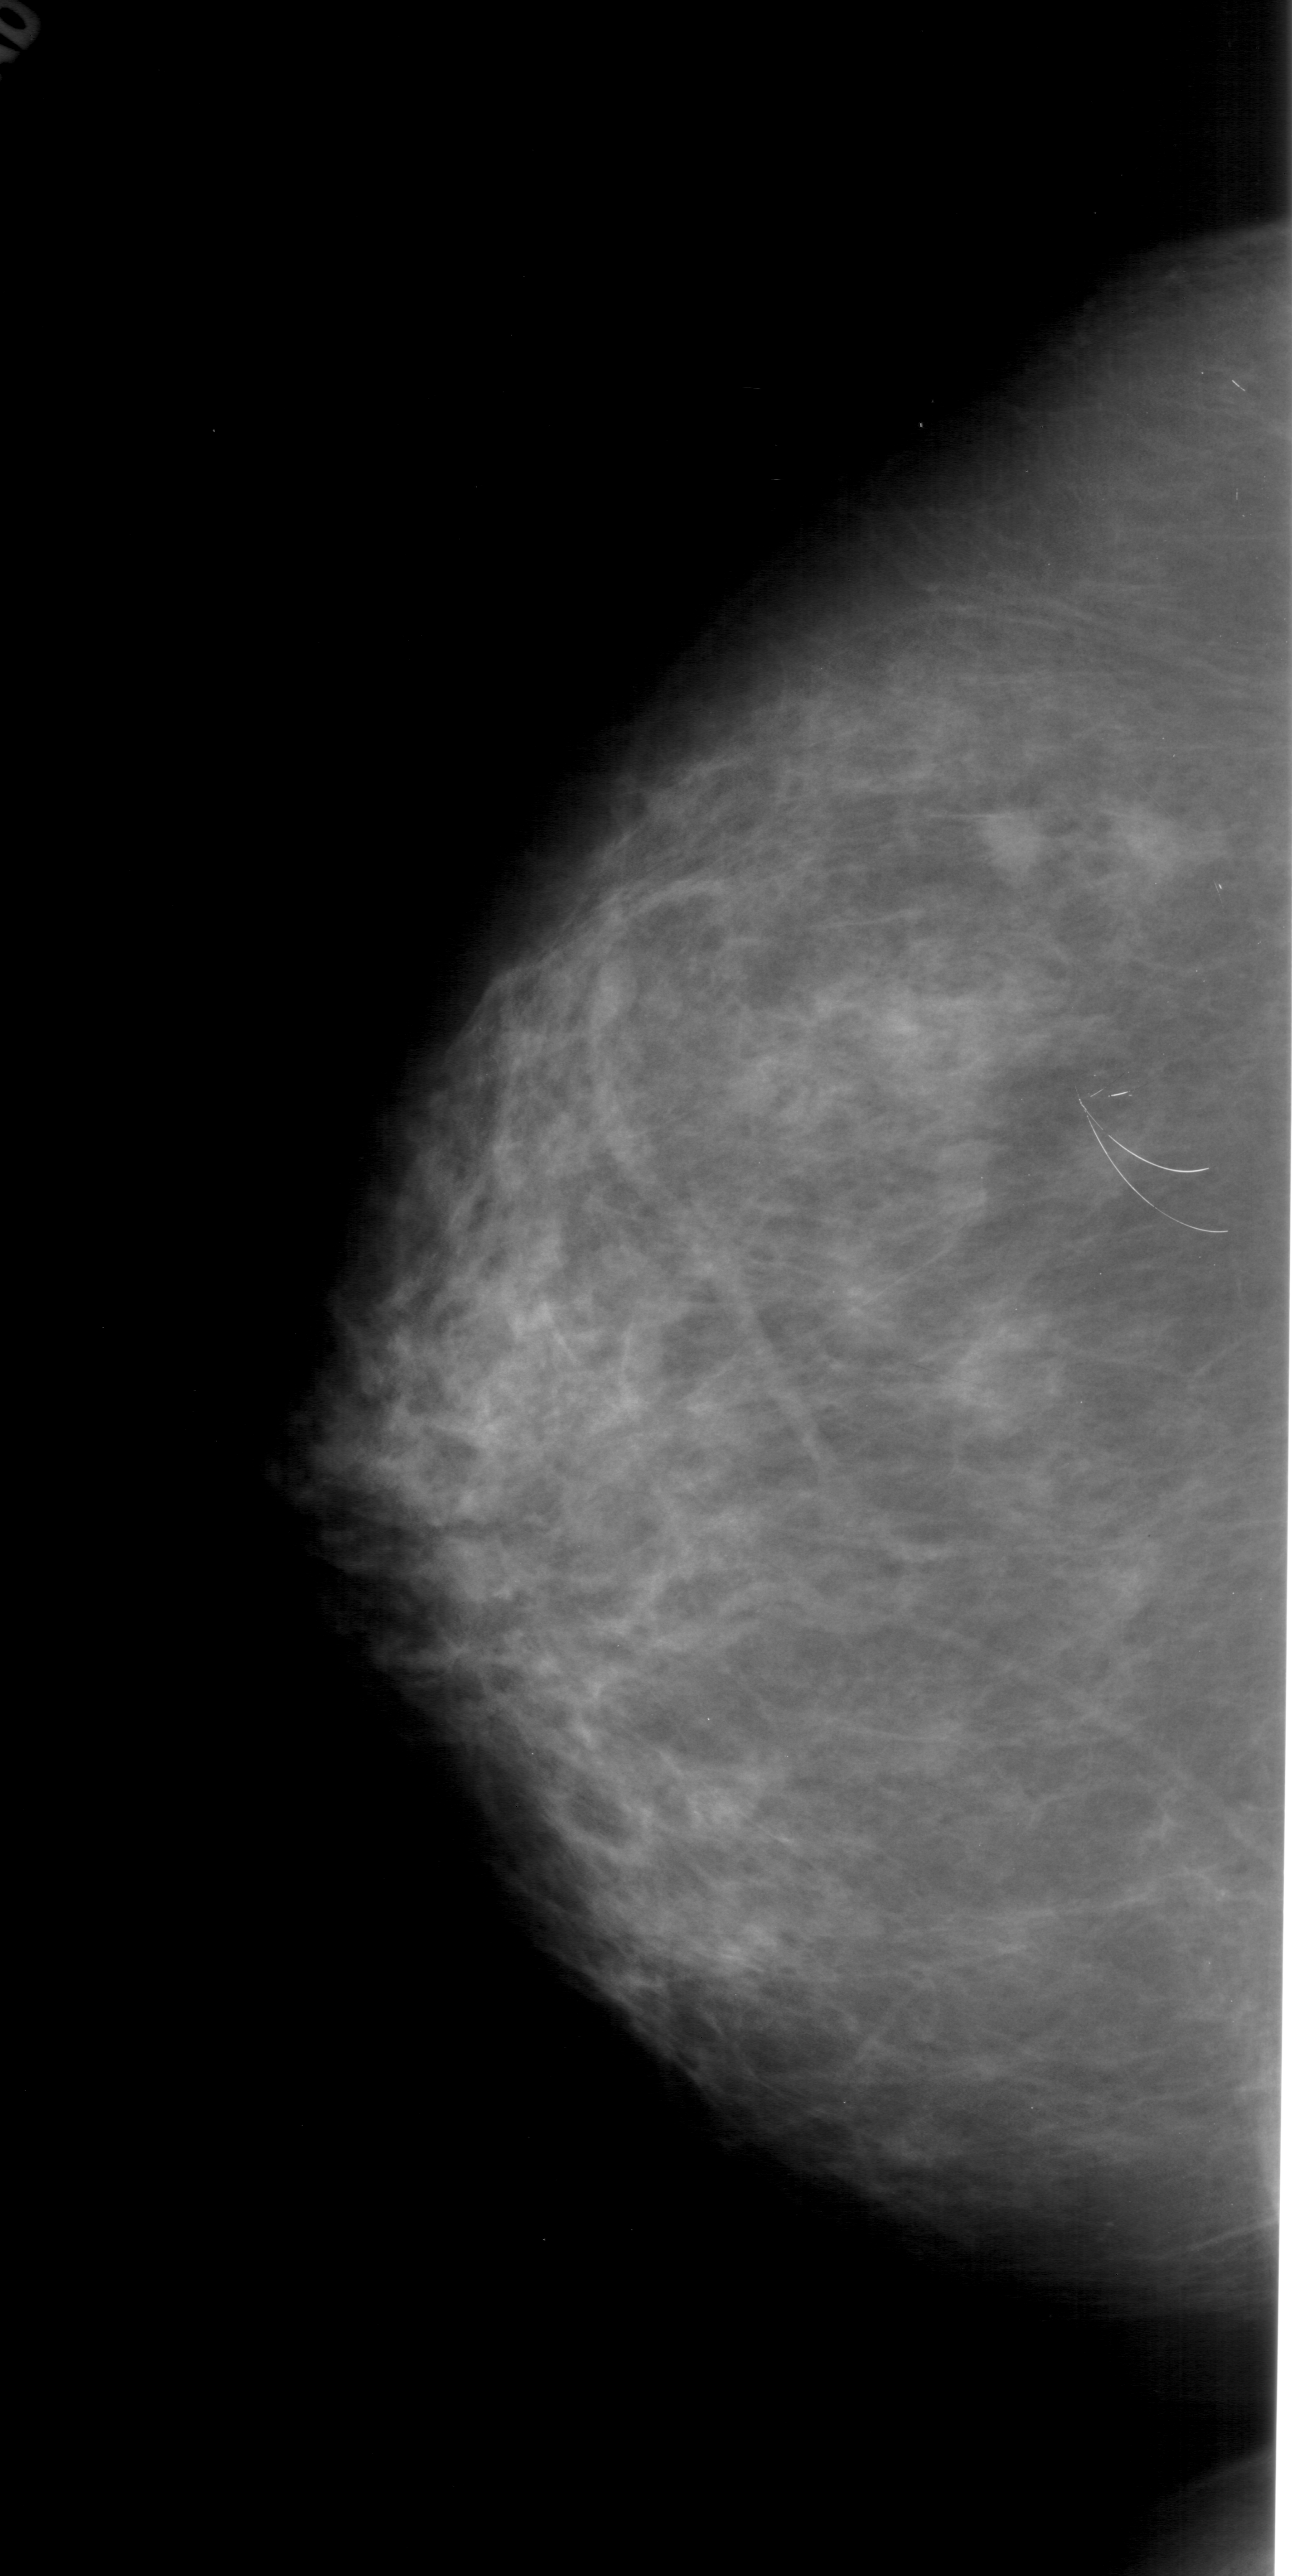
Mammogram (digitized film); left breast; craniocaudal (CC) view; BI-RADS breast density category 3 (scale 1–4); 1292 × 2576 image matrix.
Expert-marked regions of interest on this image (one box per marked abnormality):
- mass, shape irregular, margins ill defined; BI-RADS assessment category 4; pathology (as recorded): malignant: bounding box (x1, y1, x2, y2) in pixels: (1062, 791, 1215, 891)